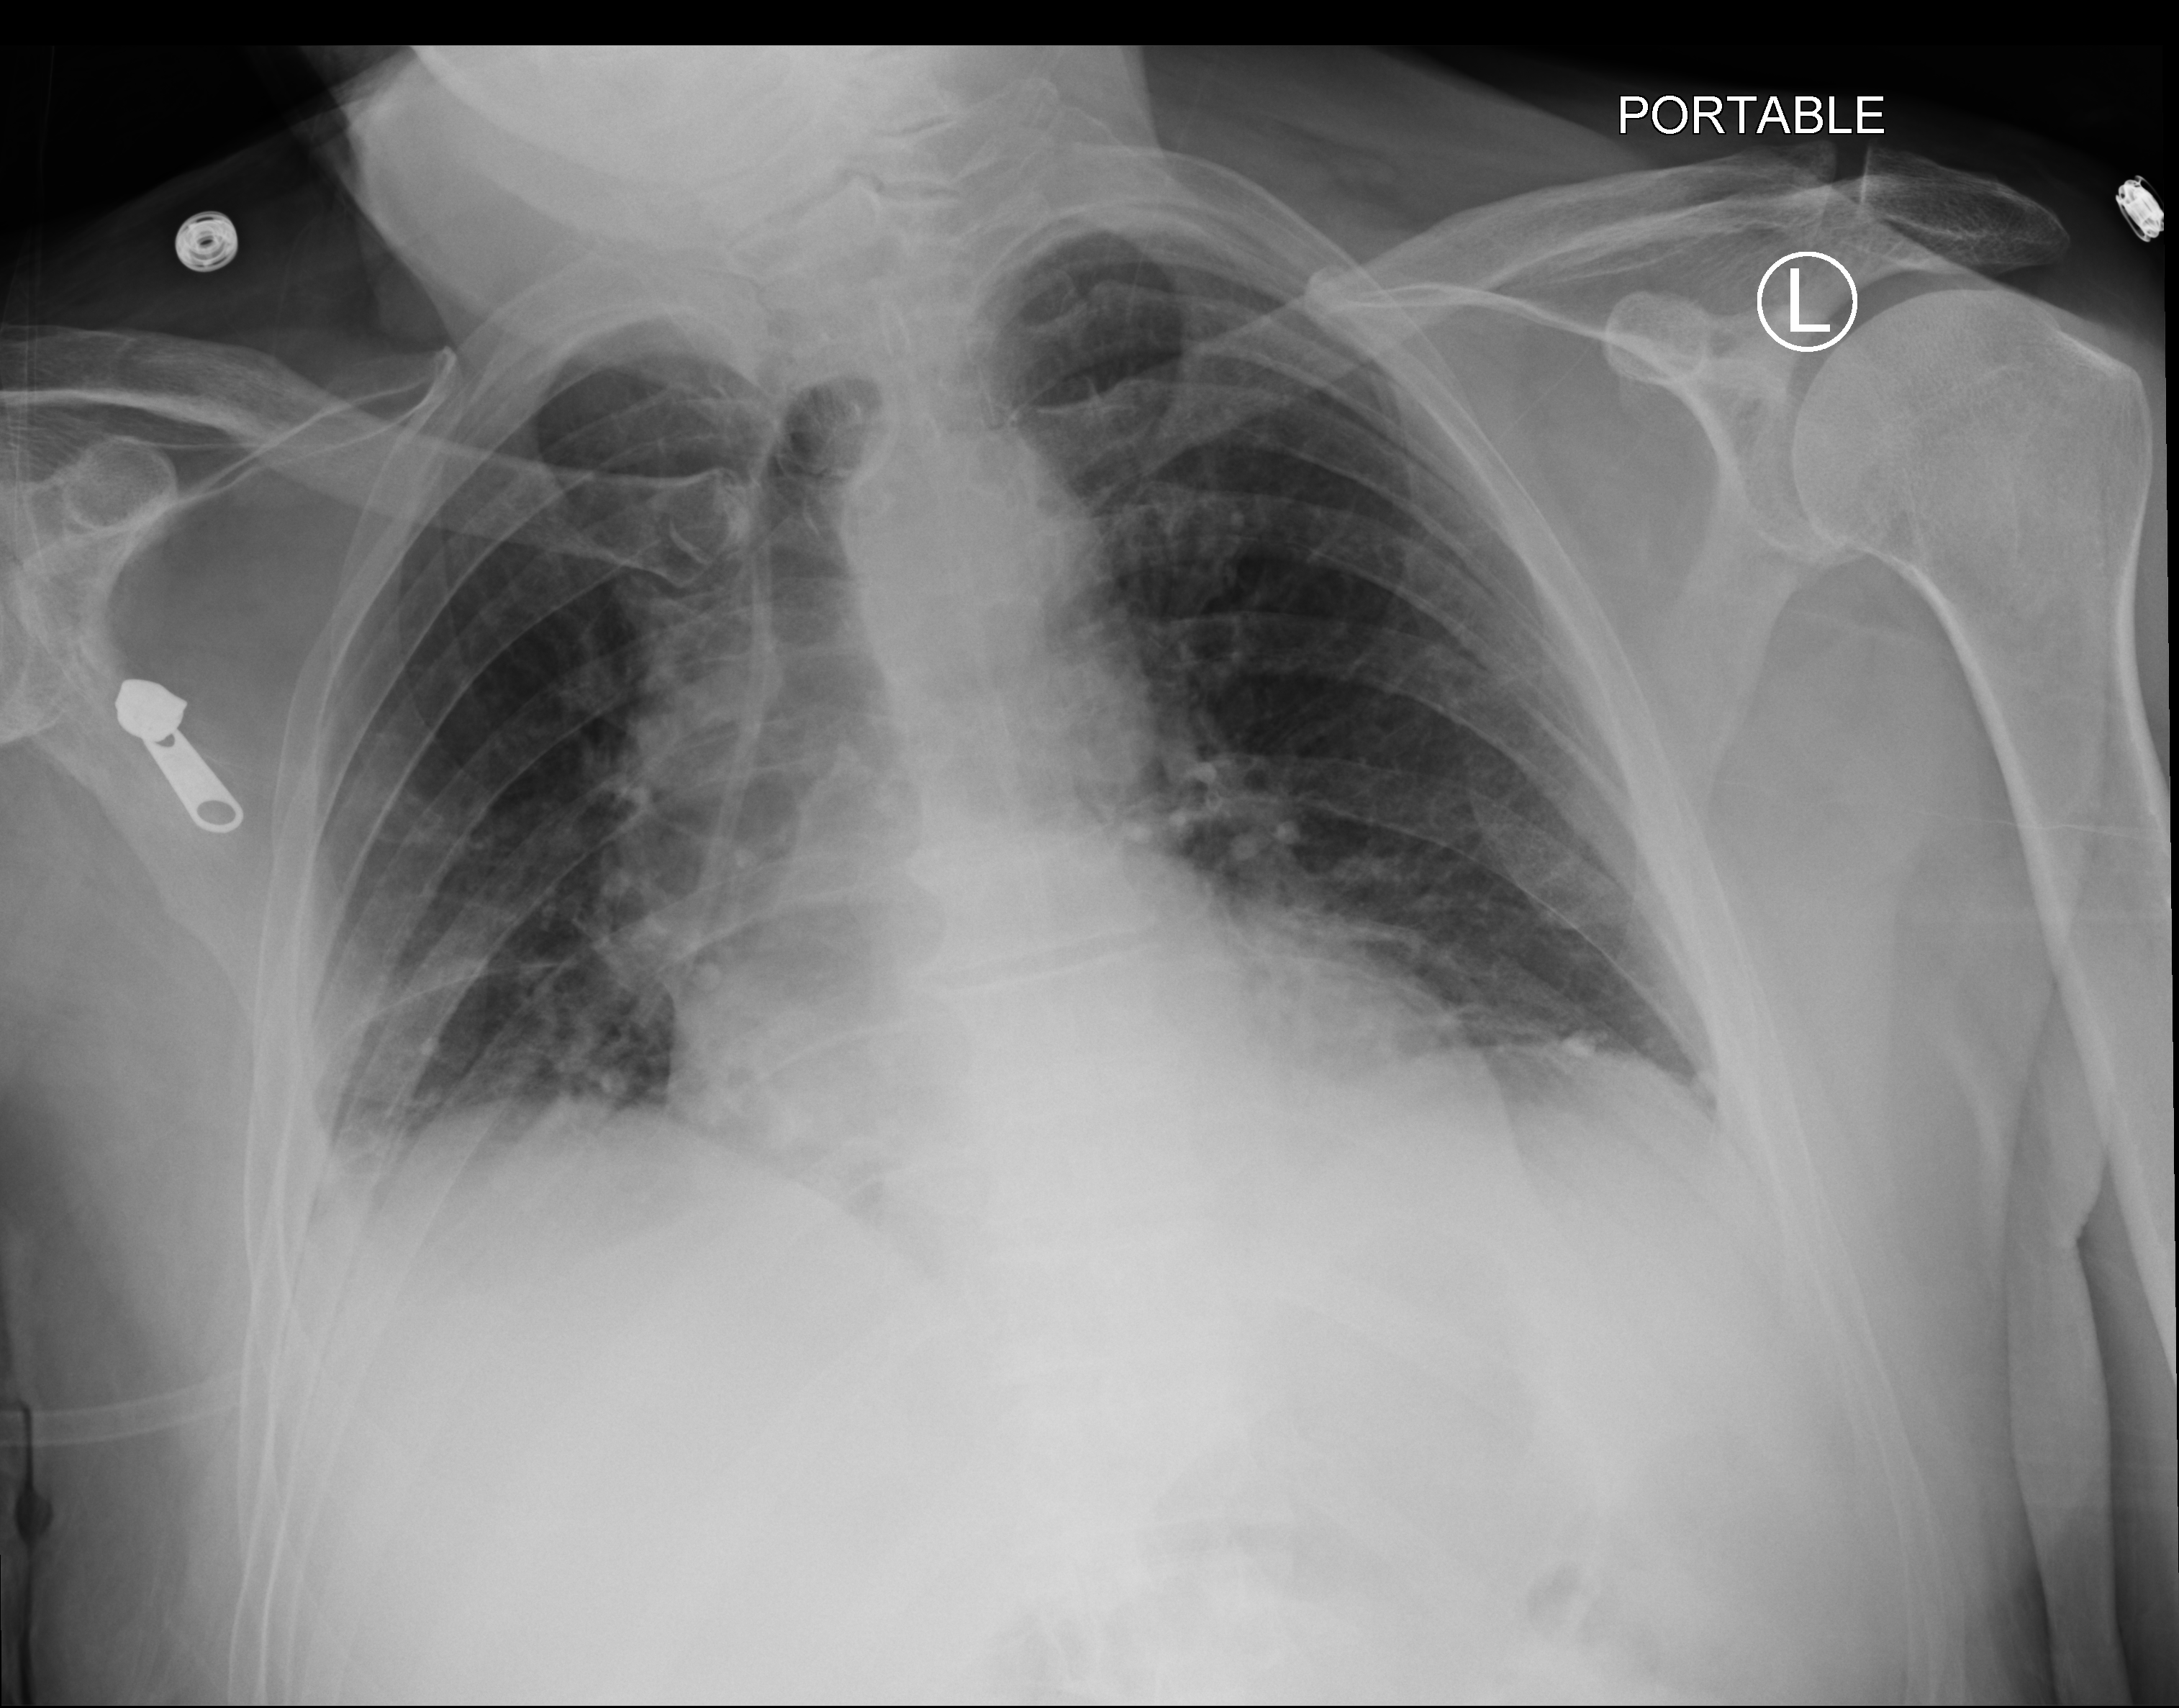
Bedside chest radiograph (computed radiography), anteroposterior (AP) projection. Patient hospitalised with COVID-19; male, aged 75–90 years.
Hospital-stay facts (about this admission, not read from this image; timing relative to this image not recorded): mechanically ventilated during this hospital stay: no; length of hospital stay: 7 days.